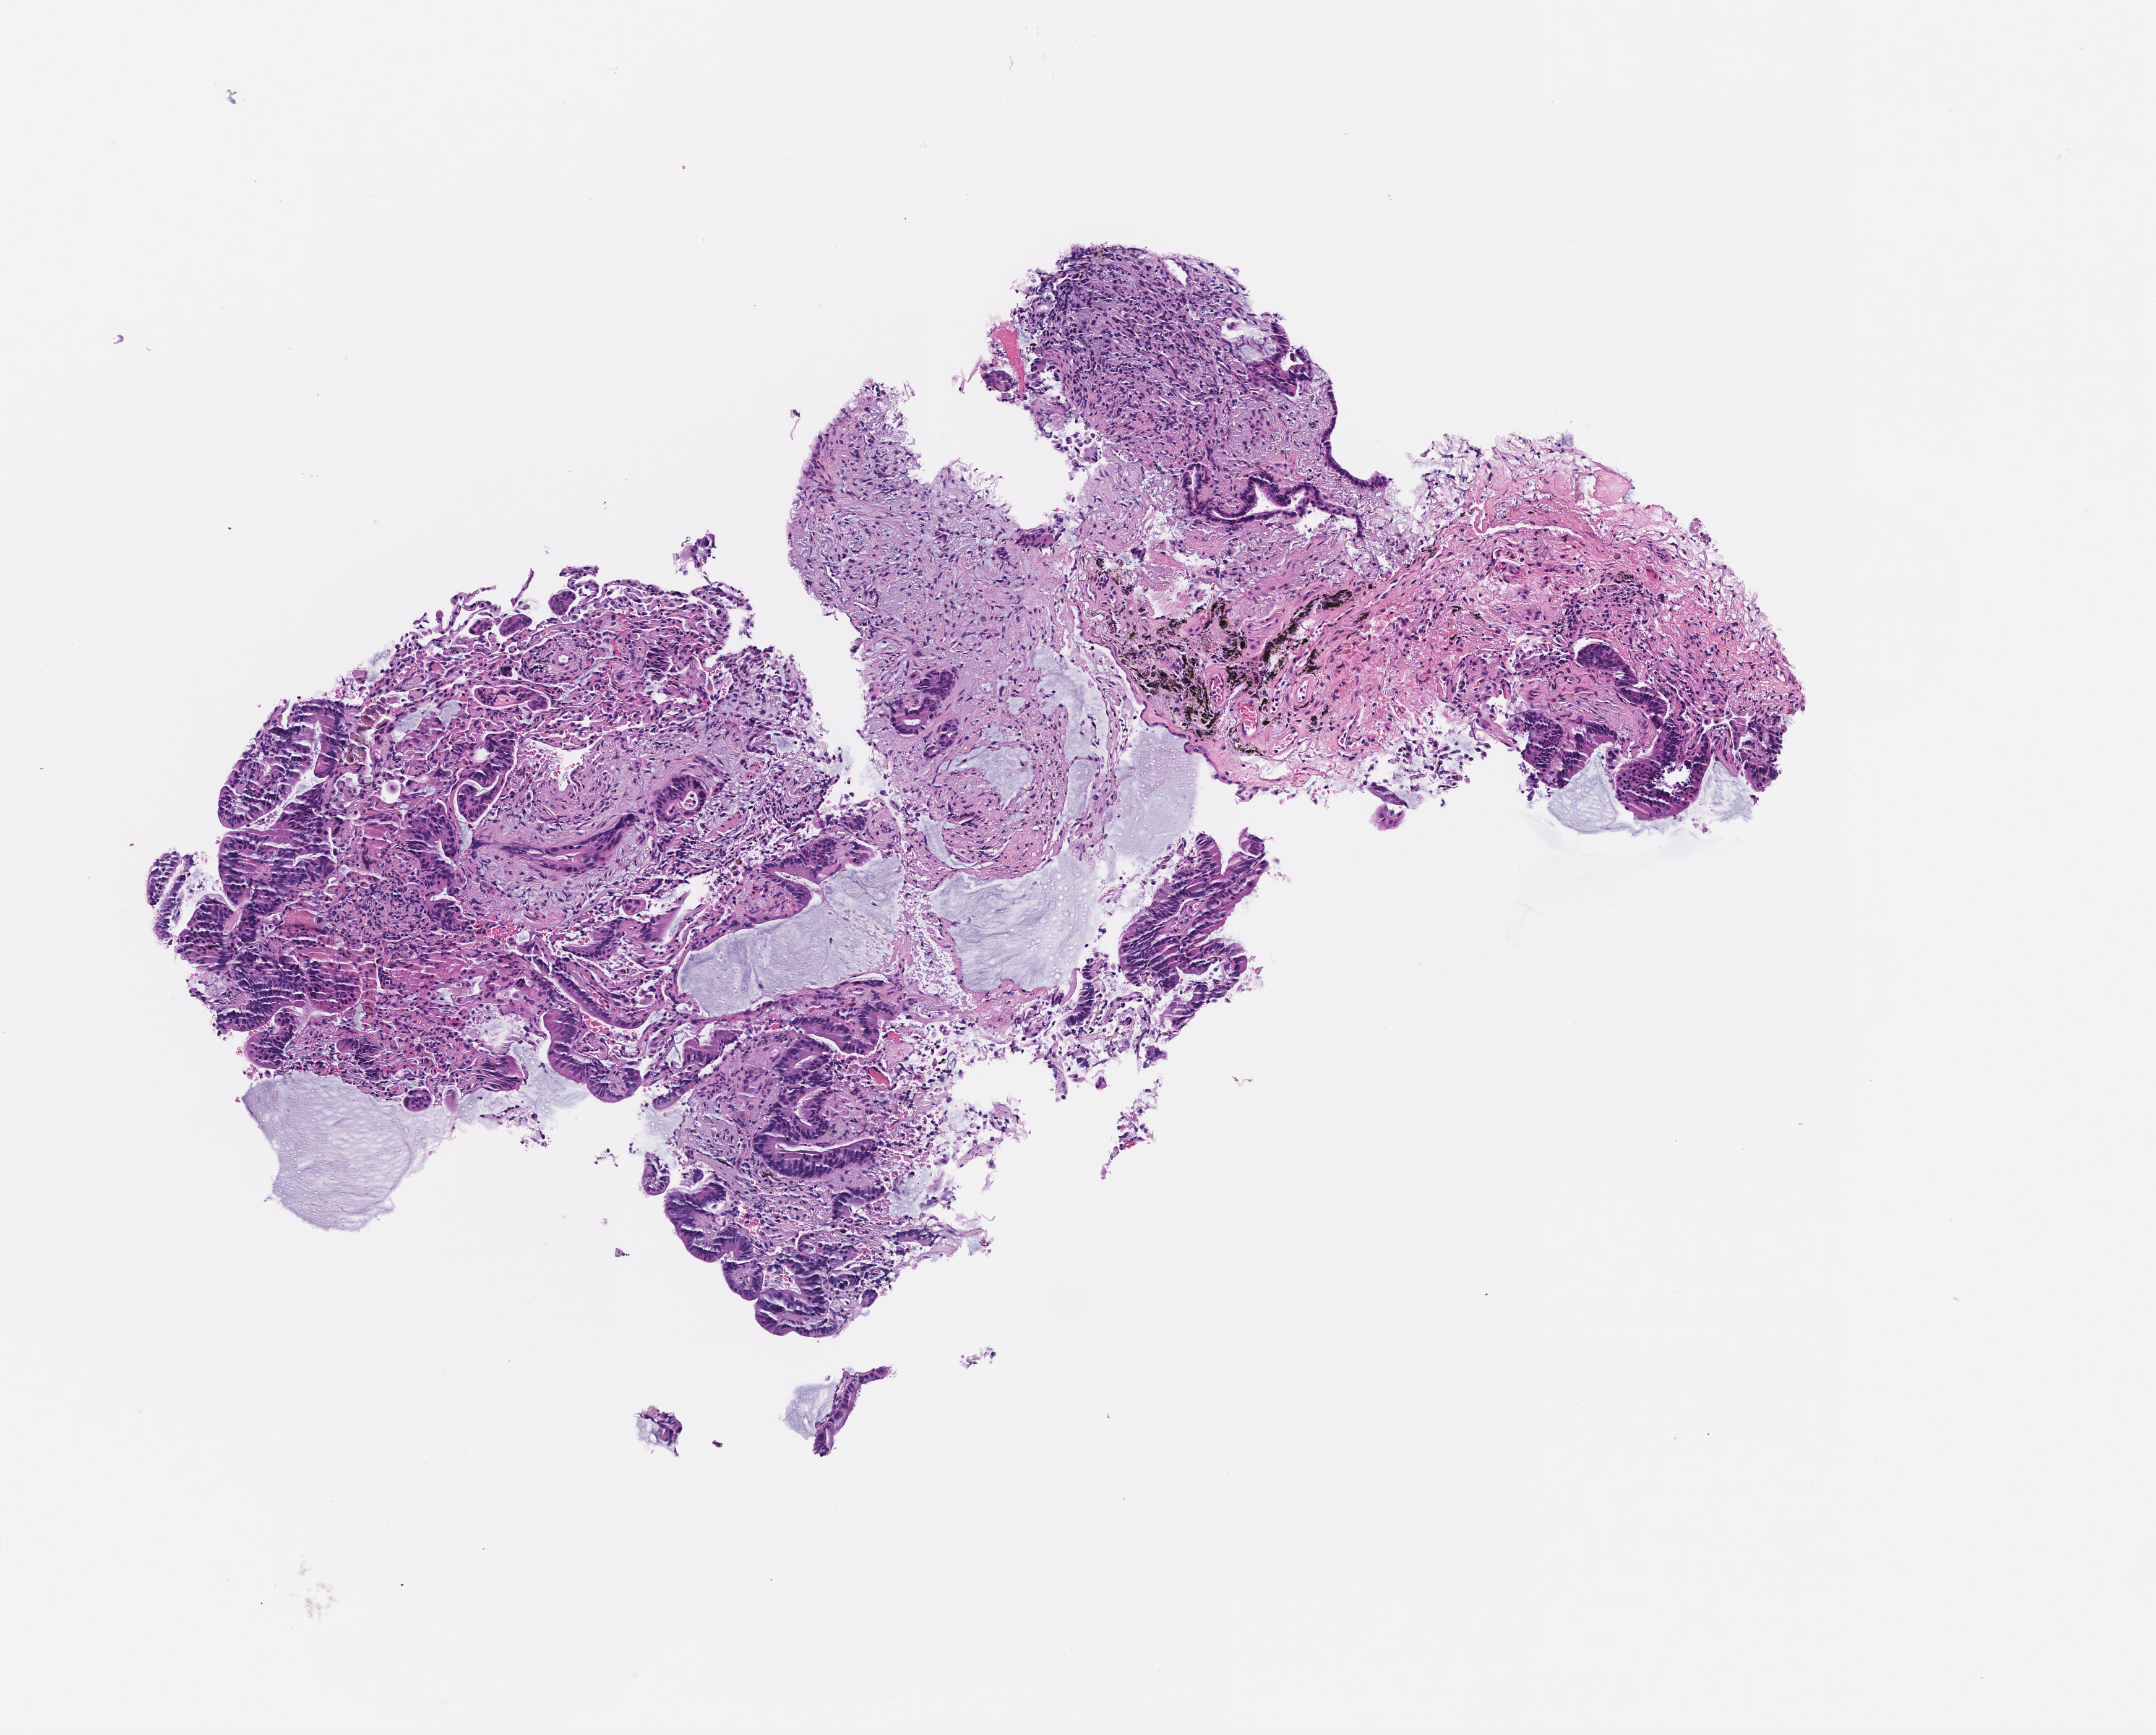
Digitized haematoxylin and eosin-stained section — low-resolution overview of the scanned area, about 3.5 x 2.8 mm; formalin-fixed, paraffin-embedded (FFPE) tissue; collected at disease progression. Patient: male.
This section: metastatic tumor tissue. Patient diagnosis (primary): Colorectal Carcinoma.